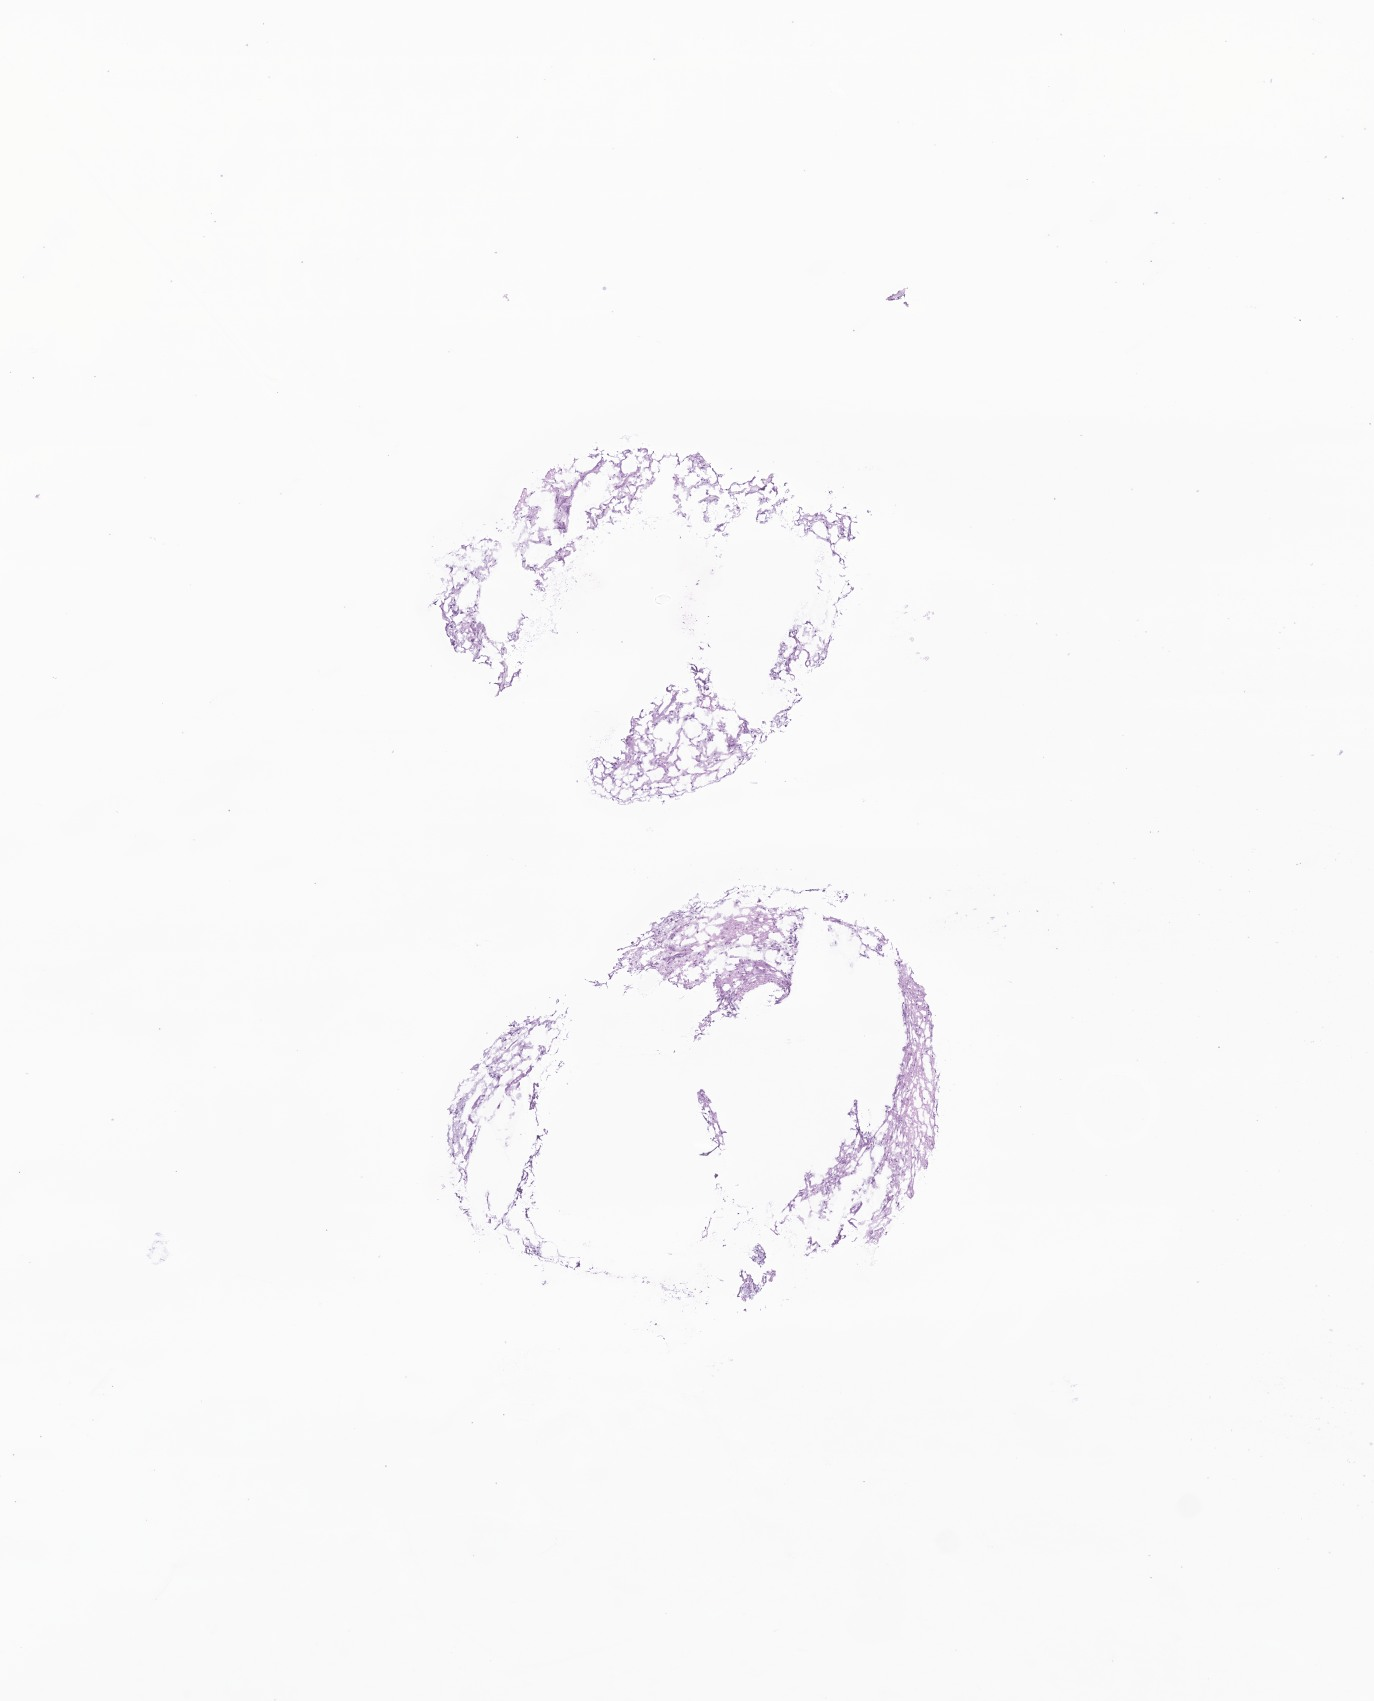
Whole-slide image, haematoxylin and eosin stain of tumor tissue from the brain — whole scanned area (about 5.8 x 7.2 mm) shown as a low-resolution overview, frozen section (OCT-embedded). Patient male; age 66 months.
Diagnosis (ICD-O-3 morphology term): Pilocytic astrocytoma.